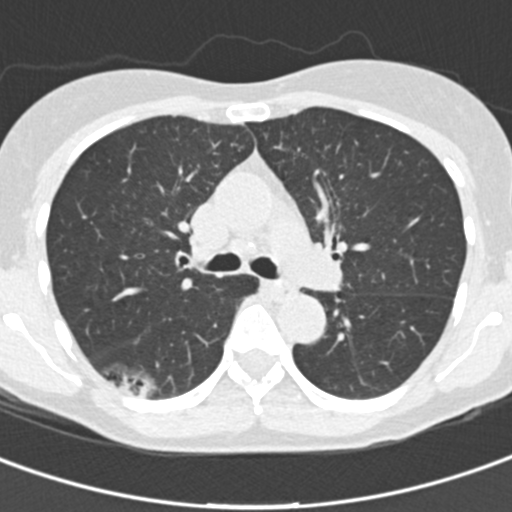
Low-dose screening chest CT, one axial slice; slice 99 of 162 in the series (ordered by position); lung window (W 1500 / L -600 HU); 2 mm slice thickness; 512 × 512 image matrix, field of view 276 × 276 mm.
Structures marked on this image (outlined manually by an expert reader):
- lesion 1 (tumor, lower lobe of right lung): bounding box [x1, y1, x2, y2] px = [136, 382, 154, 397]